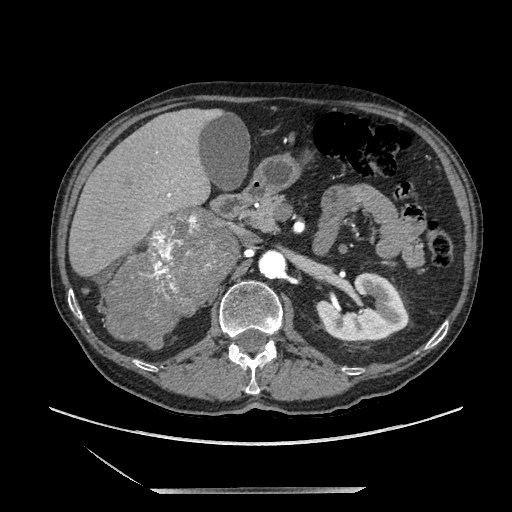
Contrast-enhanced abdominal CT, one axial slice. Slice 108 of 243 in the series (ordered by position). Soft-tissue window (W 400 / L 40 HU). 1.25 mm slice thickness. 512 × 512 image matrix. Male patient. From the clinical record (not read from this slice): diagnosis: adrenocortical carcinoma; tumour side: right adrenal; tumour size at pathology: 16 cm; Ki-67 index: 17 %; stage (as recorded): 3.
Outlined on this slice (semi-automatically segmented with operator editing):
- mass: bounding box [x1, y1, x2, y2] px = [108, 210, 232, 345]